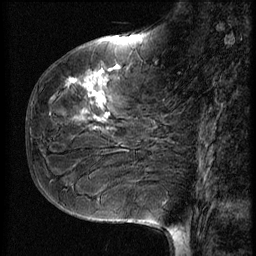
Breast MRI (dynamic contrast-enhanced), one sagittal slice; slice 23 of 56 in the series (ordered by position); 3 images stored at this slice position (order not interpretable as contrast timing); 1.5 T; TE 4.2 ms, TR 9 ms; 2.5 mm slice thickness; 256 × 256 image matrix, field of view 180 × 180 mm. Patient: female, 51 years. From the clinical record (not read from this slice): setting: breast cancer imaged before/during neoadjuvant chemotherapy; receptor status: HR-positive, HER2-negative.
Annotated regions visible in this slice (semi-automatic segmentation, software-assisted and operator-edited):
- analysis volume of interest (the breast-tissue region the enhancement analysis was run in; not a lesion): bounding box (x1, y1, x2, y2) in pixels: (41, 58, 167, 161)
- tumour enhancement mask (voxels above the 140 % enhancement threshold inside the analysis volume of interest): (68, 70, 109, 122)